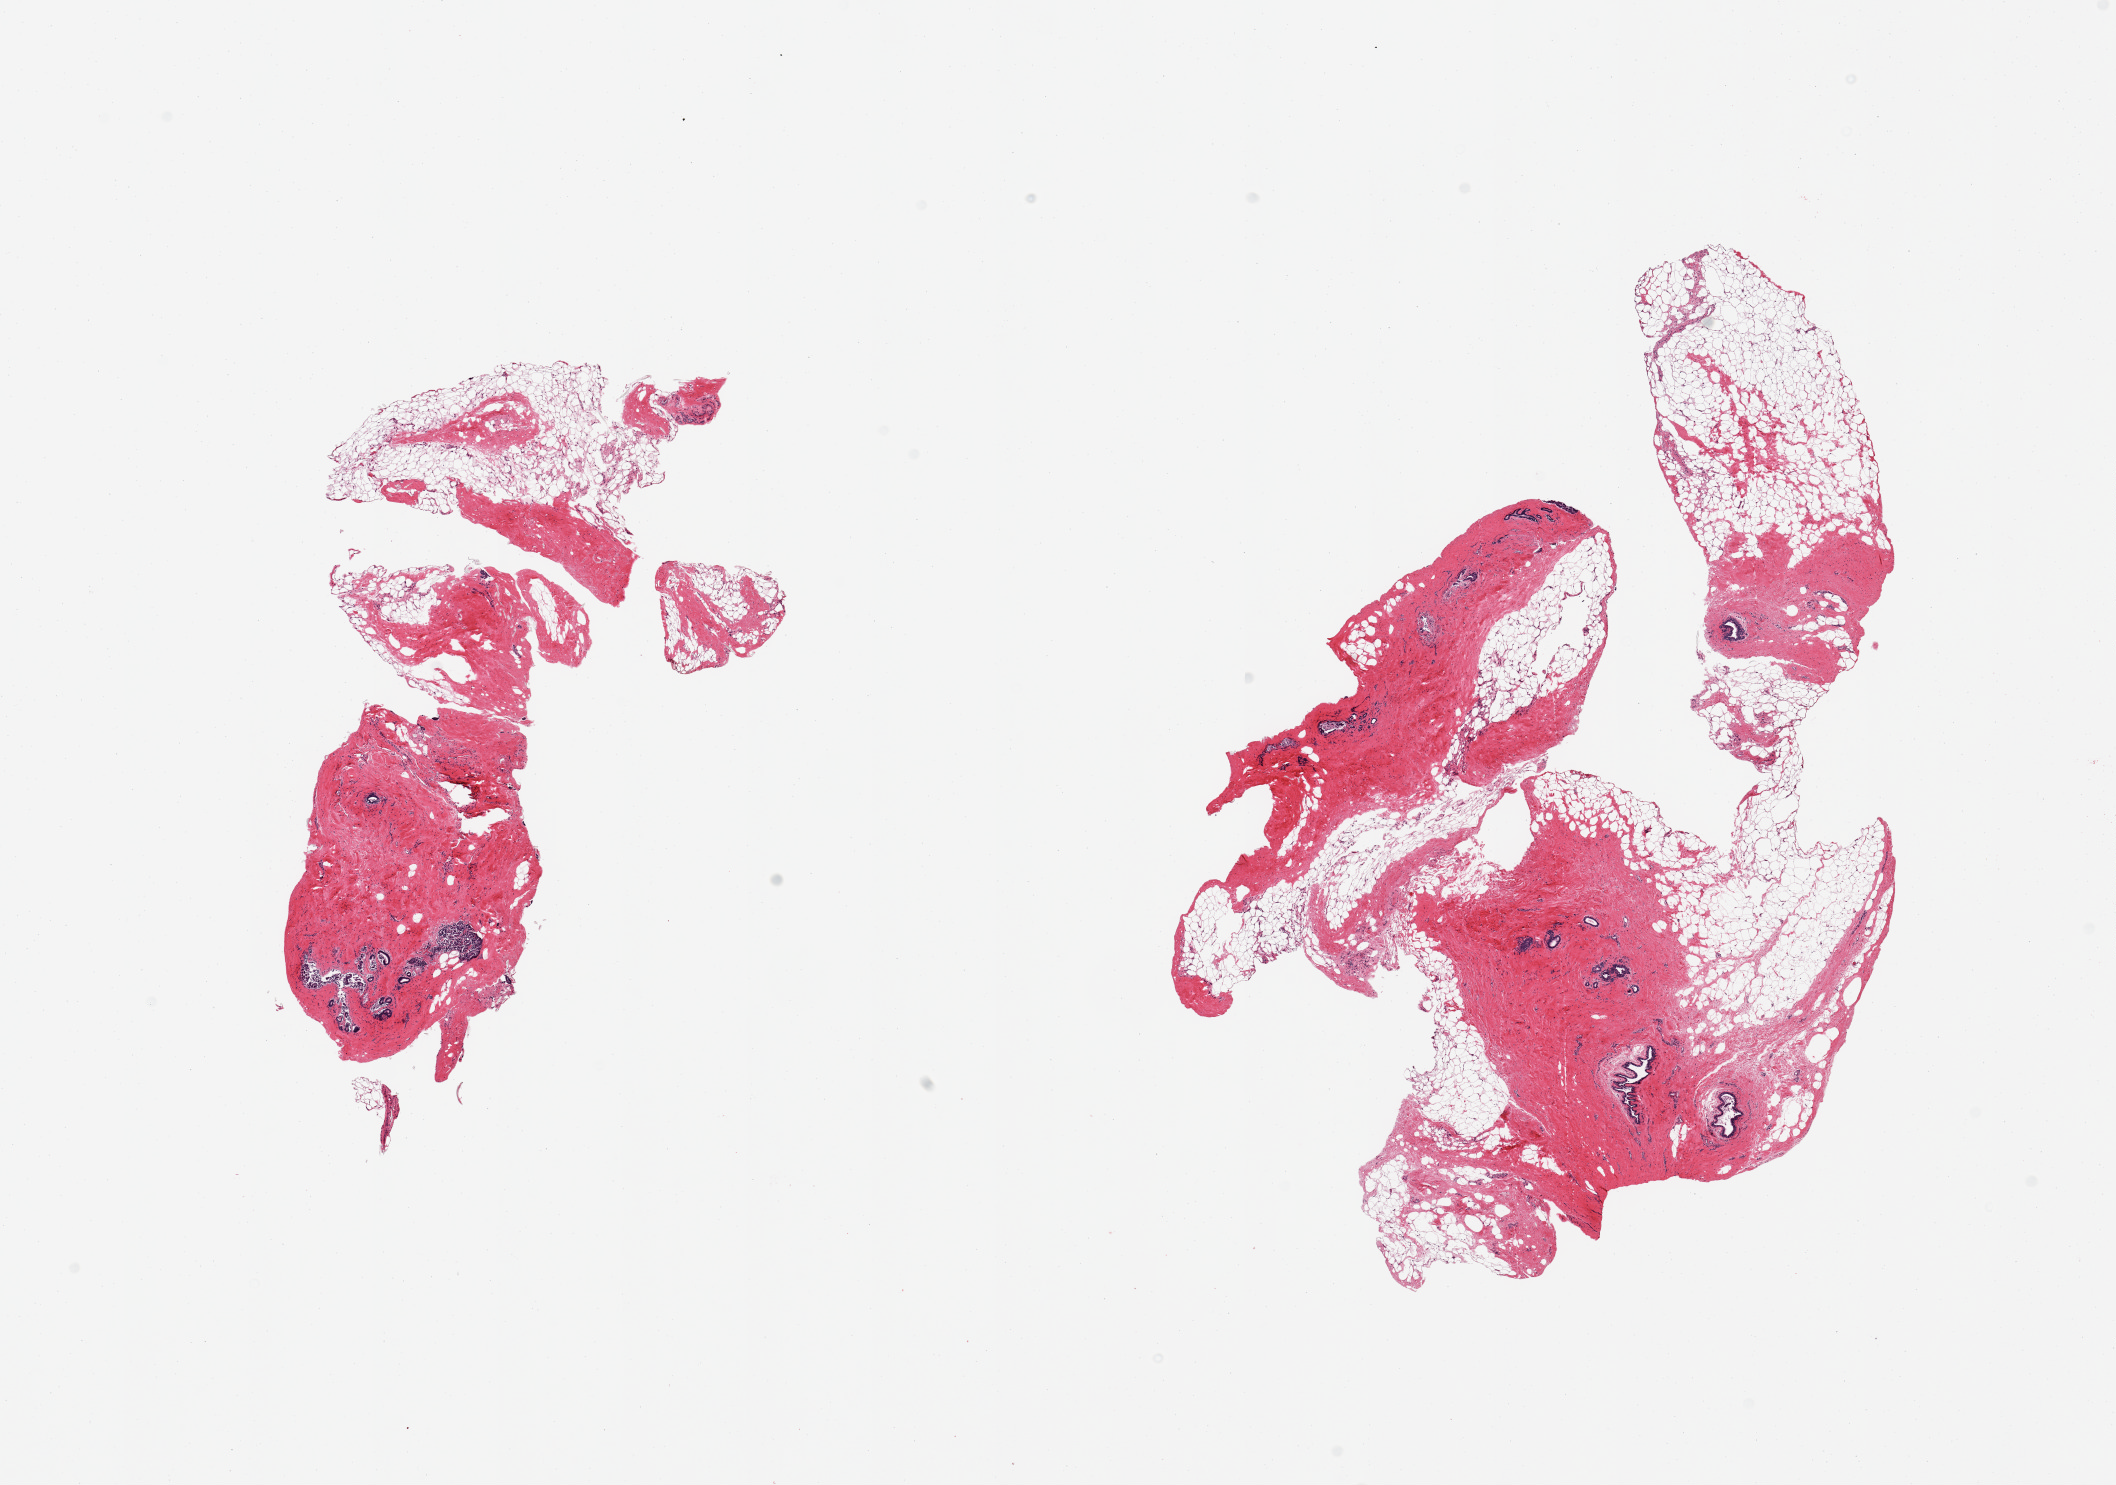
Digitized hematoxylin and eosin (H&E)-stained section, whole scanned area (about 16.7 x 11.7 mm) shown as a low-resolution overview. PAXgene-fixed, paraffin-embedded tissue. Sampled site (target tissue): breast. Tissue donor sample. Female donor.
Review note (as recorded): 2 pieces, ductal lobular elements present.